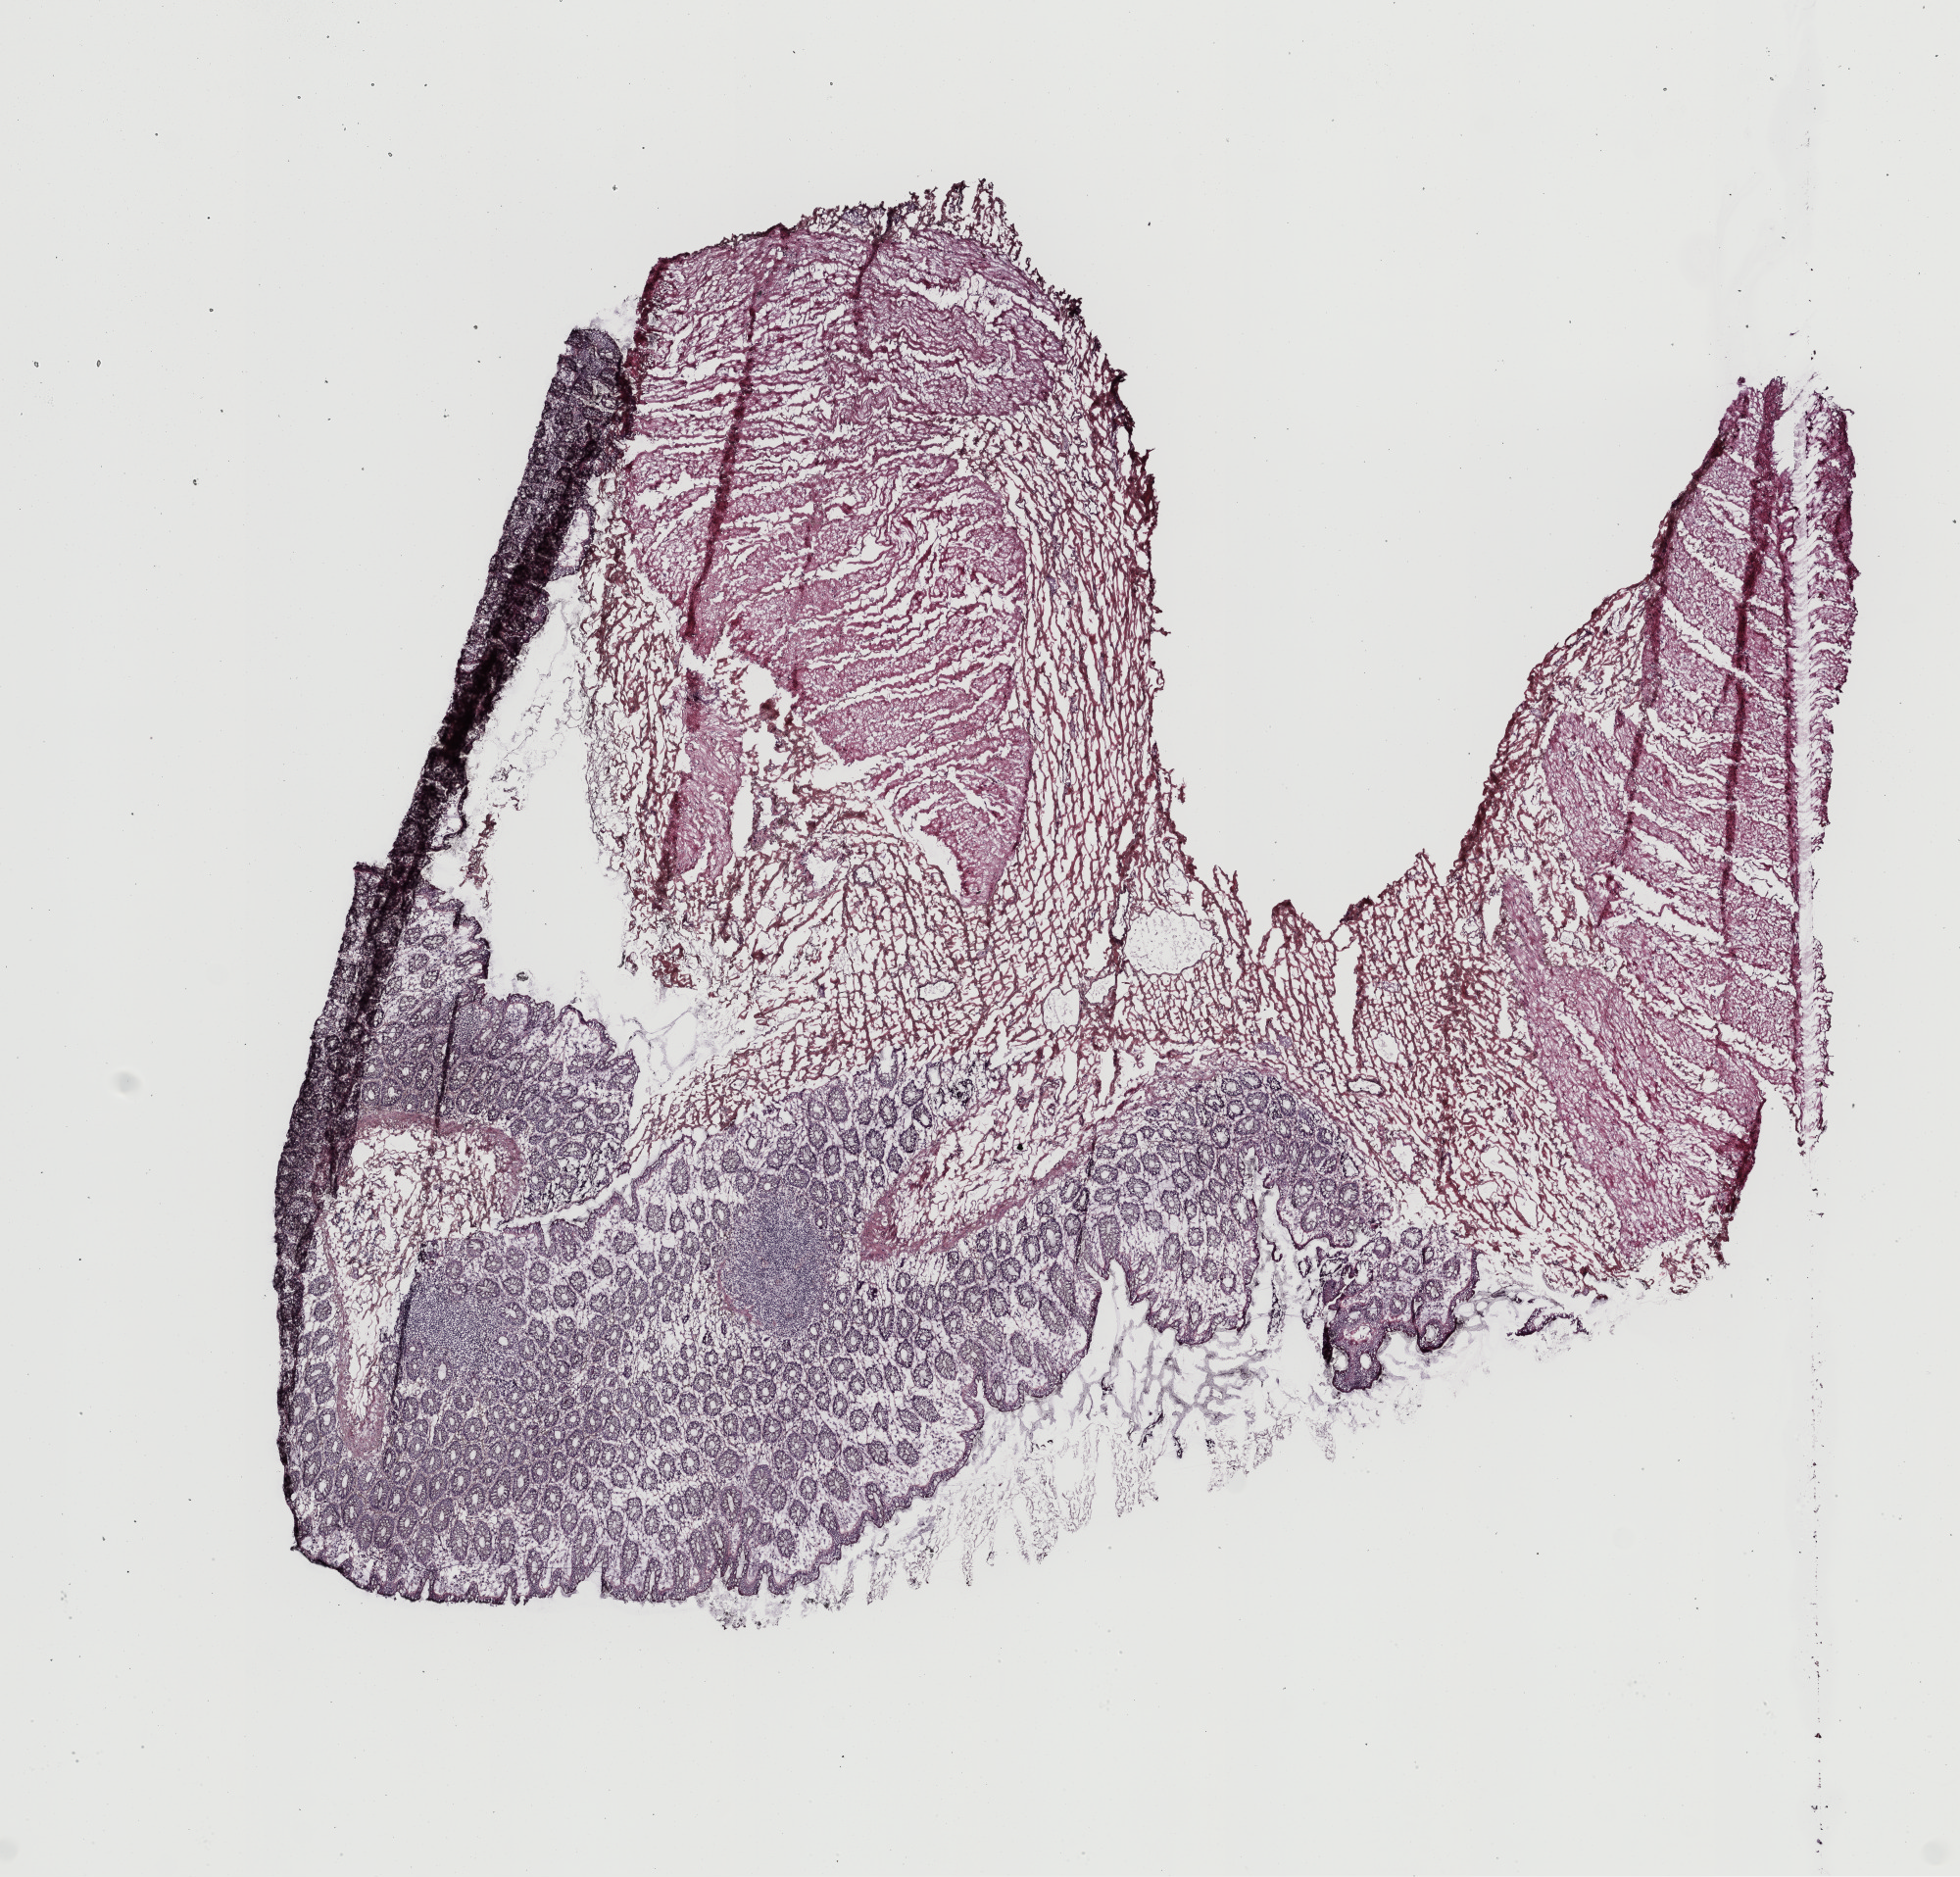
Digitized H&E-stained tissue section (whole slide) — whole scanned area (about 8.0 x 7.7 mm) shown as a low-resolution overview, frozen section from the top of the tissue portion, colon, solid tissue normal (non-tumour tissue) sample. Patient: male, age at initial diagnosis 68 years.
This section: solid tissue normal sample (biorepository sample class). Patient diagnosis: Adenocarcinoma, NOS (sigmoid colon).